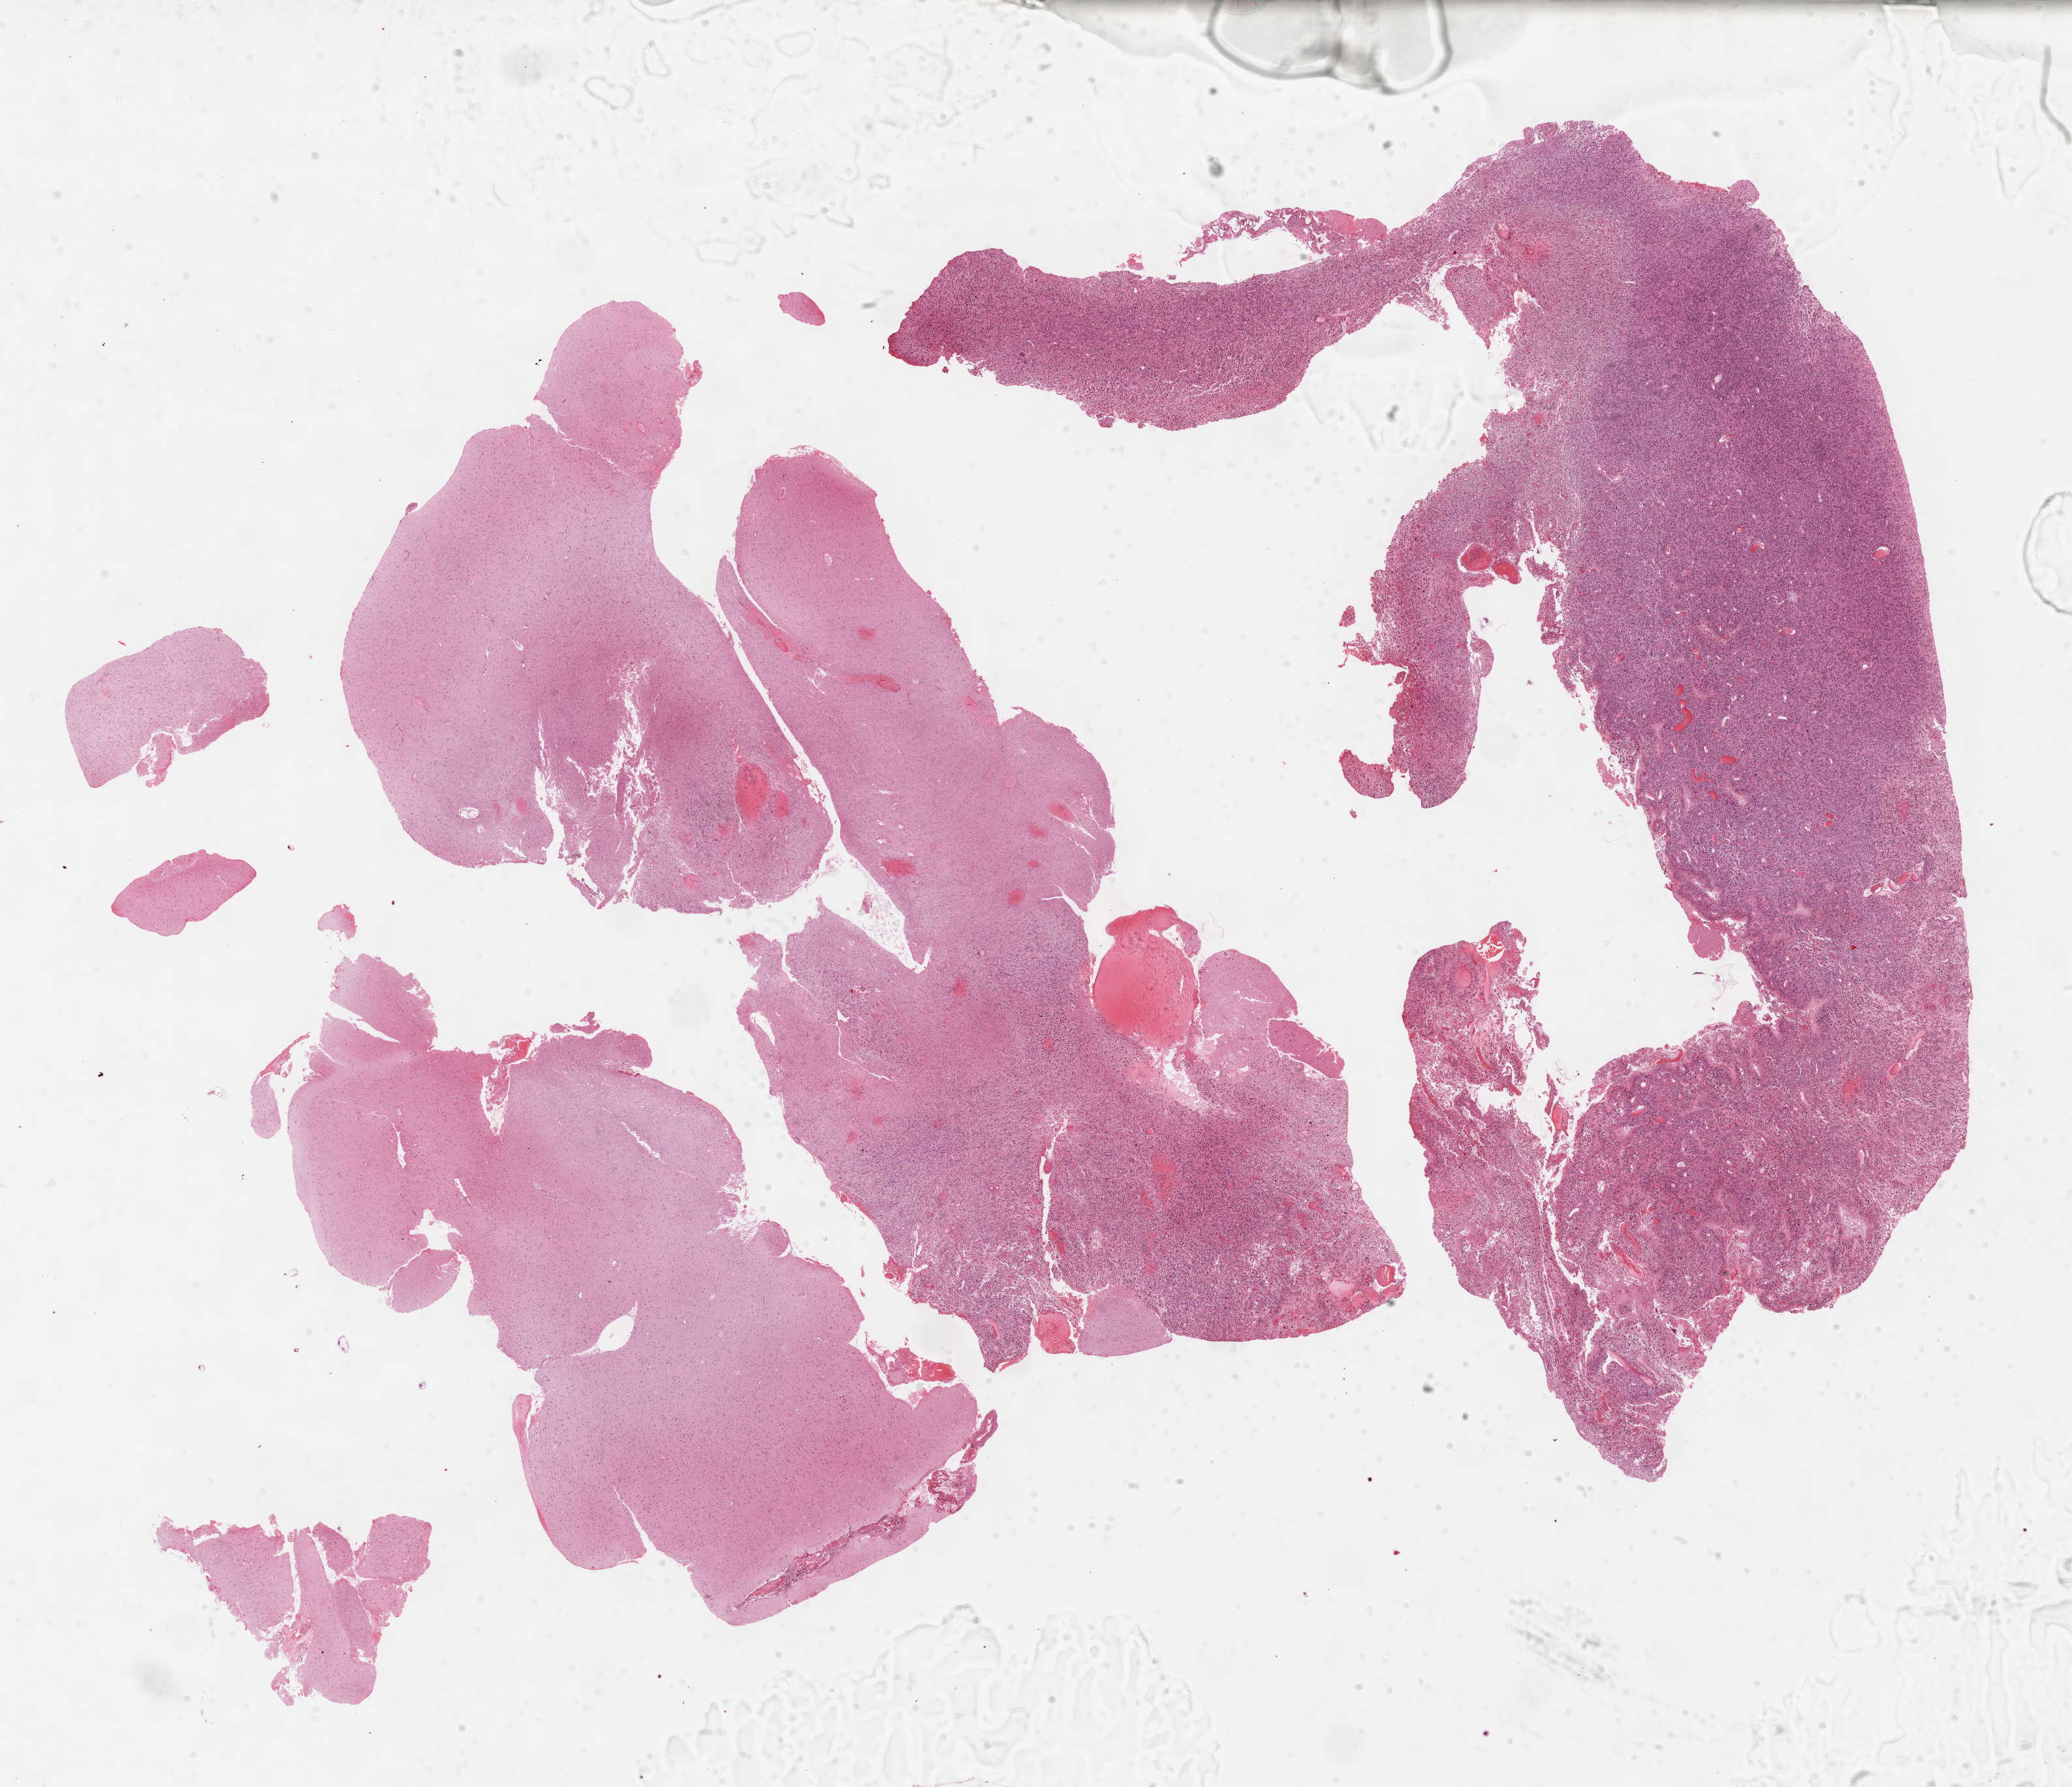
H&E-stained whole-slide image — whole scanned area (about 25.7 x 22.1 mm) shown as a low-resolution overview; formalin-fixed paraffin-embedded (FFPE) diagnostic section; sample: primary tumour, brain. Male patient; age at initial diagnosis 48 years.
Diagnosis: Glioblastoma.